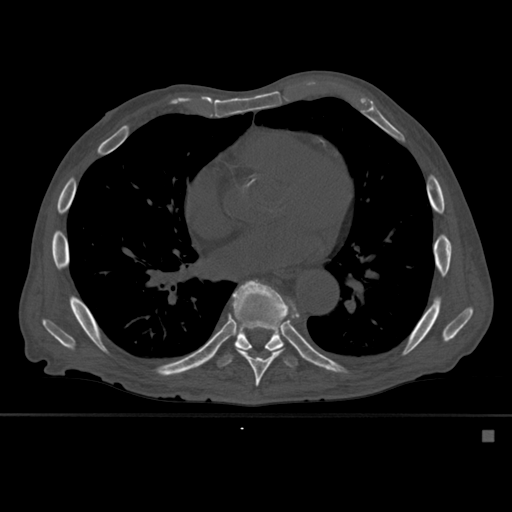
CT including the spine, one axial slice. Slice 343 of 527 in the series (ordered by position). Bone window (W 1800 / L 400 HU). 512 × 512 image matrix, field of view 373 × 373 mm. Patient: male, 78 years. Case-level facts recorded for this patient, not image findings: primary cancer: prostate.
Annotated regions visible in this slice (semi-automatic segmentation, software-assisted and operator-edited):
- T8 vertebra: box from (x=229, y=280) to (x=299, y=387) px
- T9 vertebra: (x=217, y=287)–(x=298, y=369)